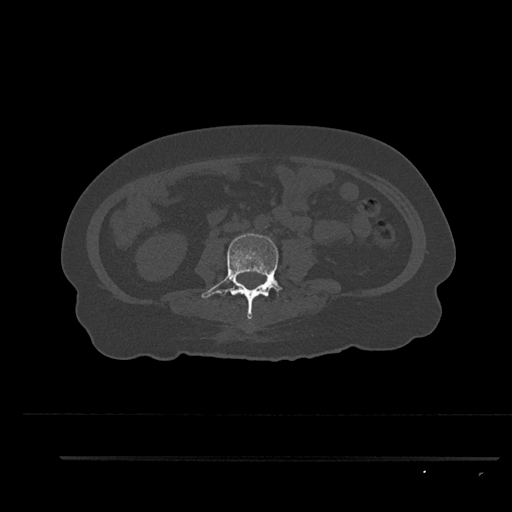
CT including the spine, one axial slice; position 86 of 797 along the scan axis; reconstruction kernel Br40s/3; bone window (W 1800 / L 400 HU); 0.5 mm slice thickness; 512 × 512 image matrix, field of view 408 × 408 mm. Female patient, age 44 years. From the clinical record (not read from this slice): primary cancer: renal; vertebrae with lytic lesions (as recorded): L1.
Structures marked on this image (semi-automatically segmented with operator editing):
- L3 vertebra: bounding box [x1, y1, x2, y2] px = [202, 233, 291, 319]